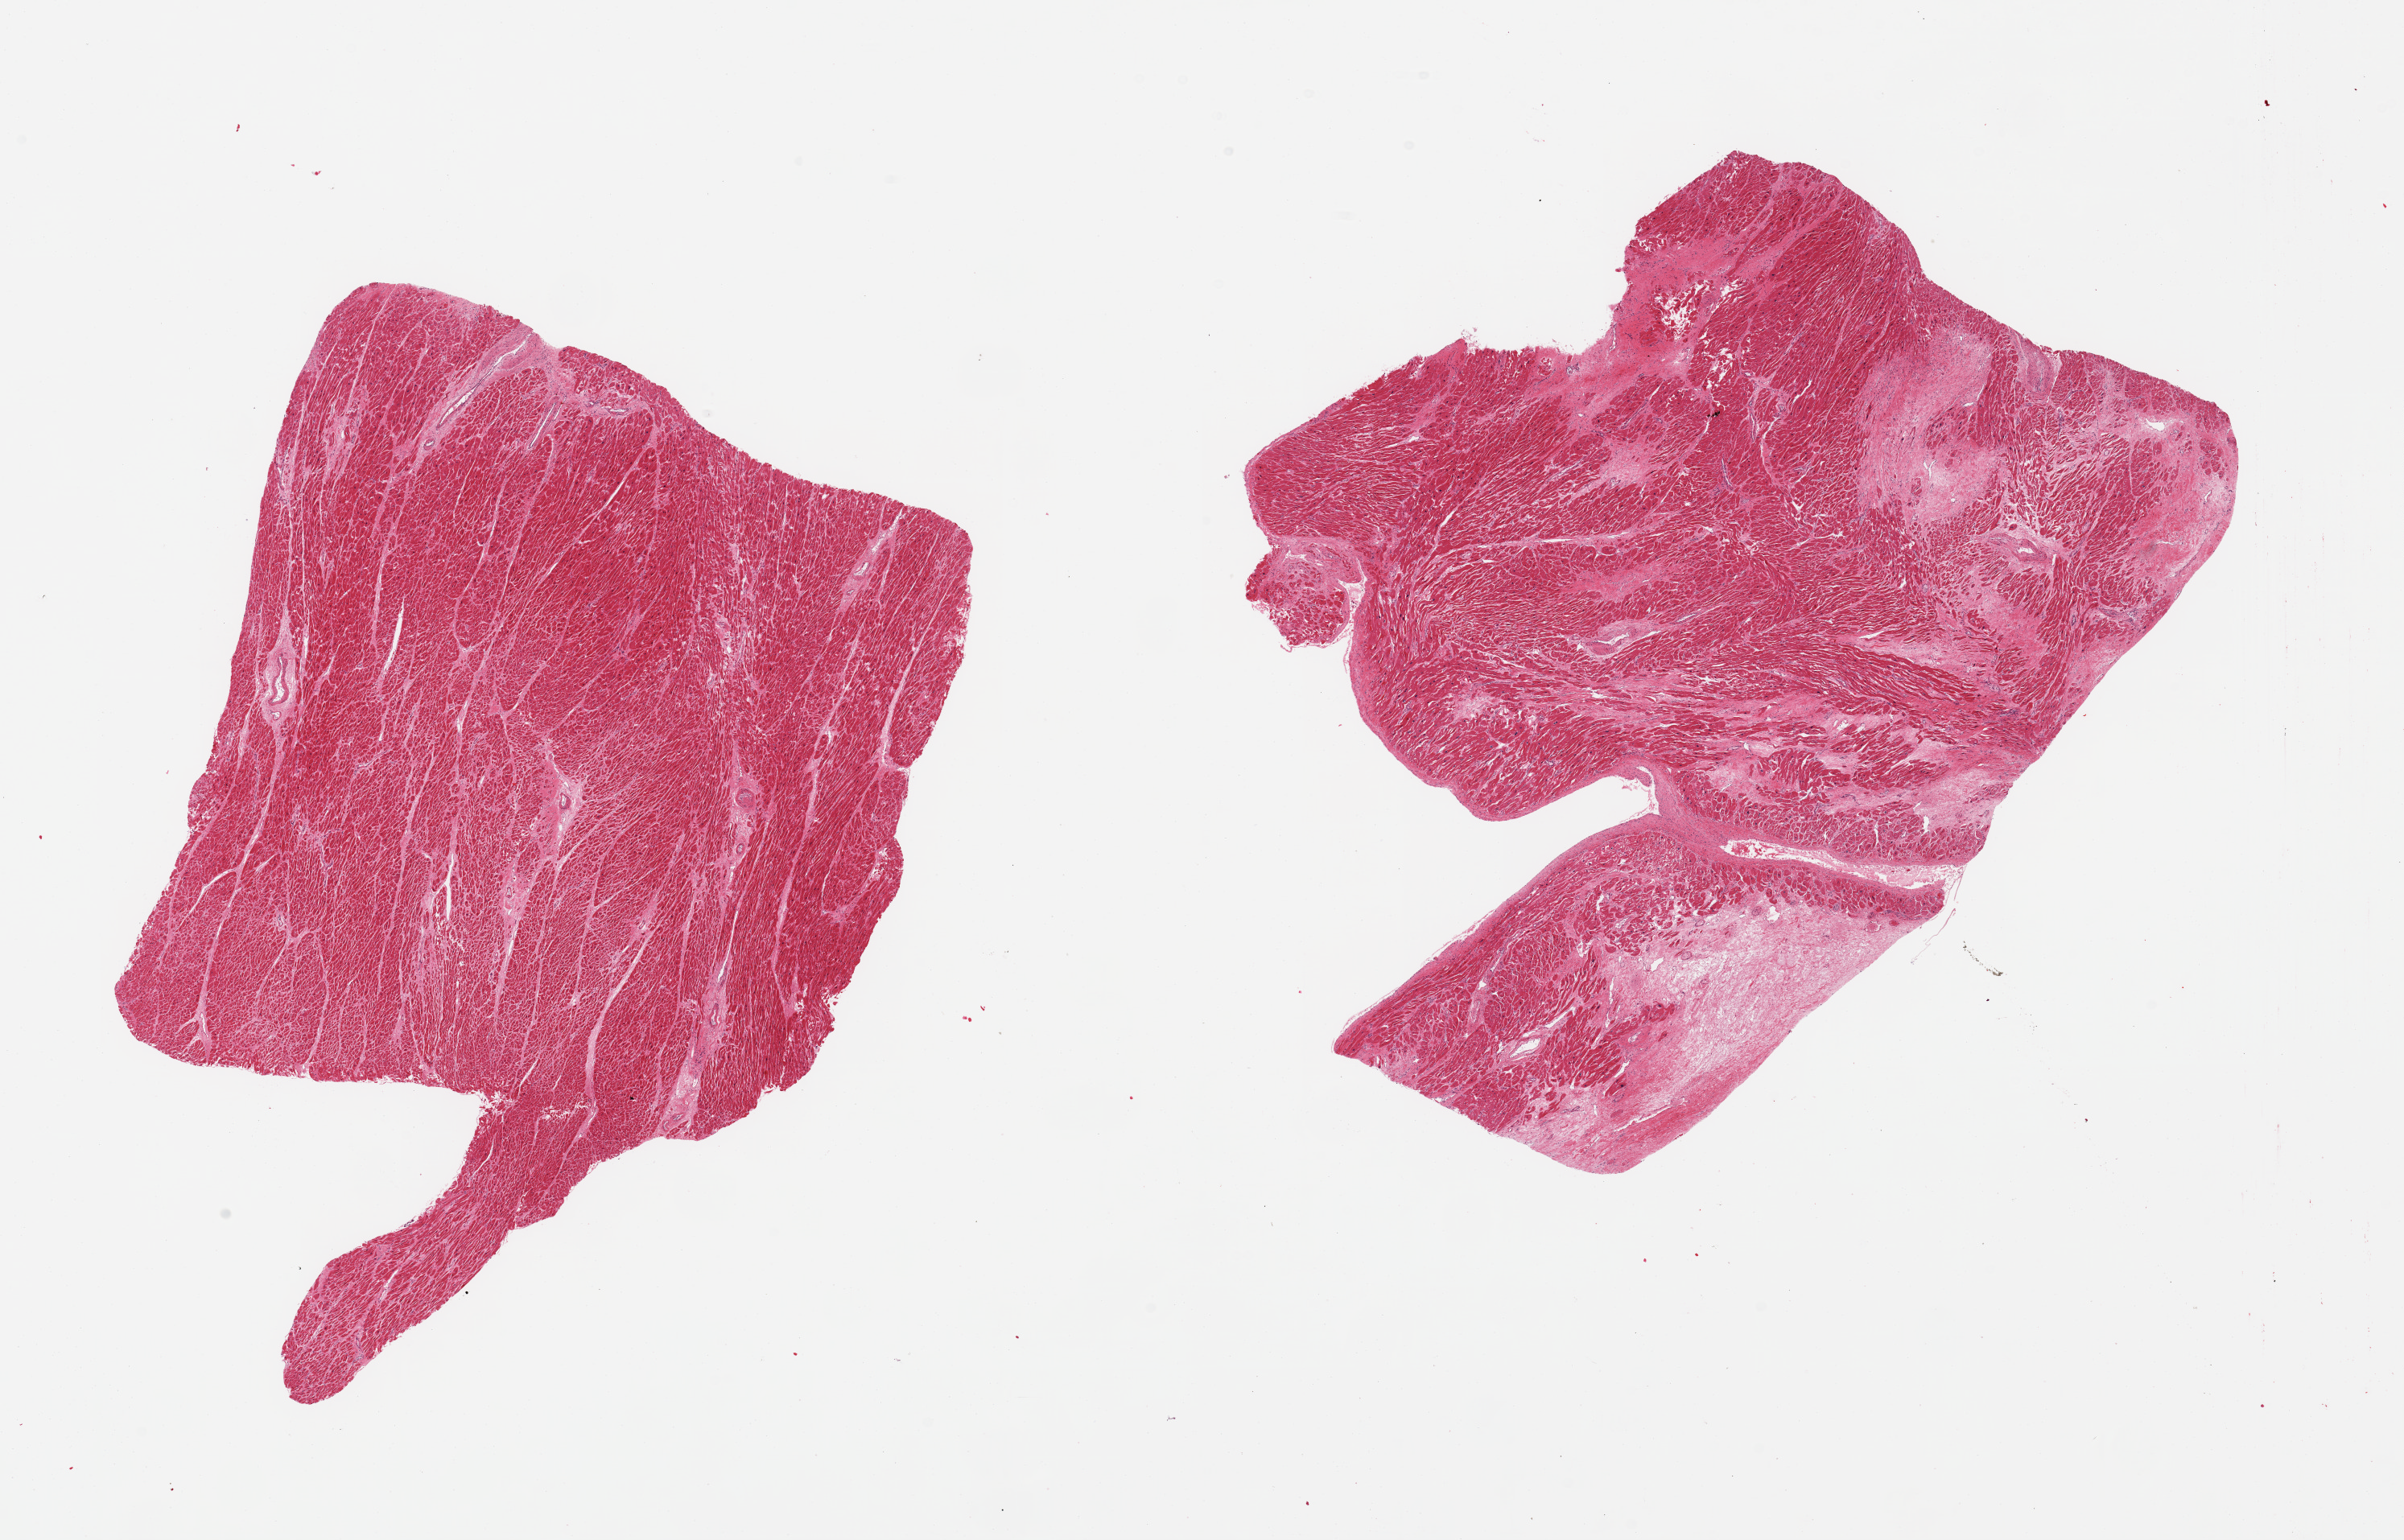
Whole-slide image, haematoxylin and eosin stain, shown as a low-resolution overview of the whole scanned area (about 23.6 x 15.1 mm). PAXgene-fixed paraffin-embedded (PFPE) section. Sampled site (target tissue): heart. Donor tissue sample. Female donor.
• review note (as recorded): 1 pieces: 1 with extensive (30%) scar content, other with <5% scar; consistent with old infarction